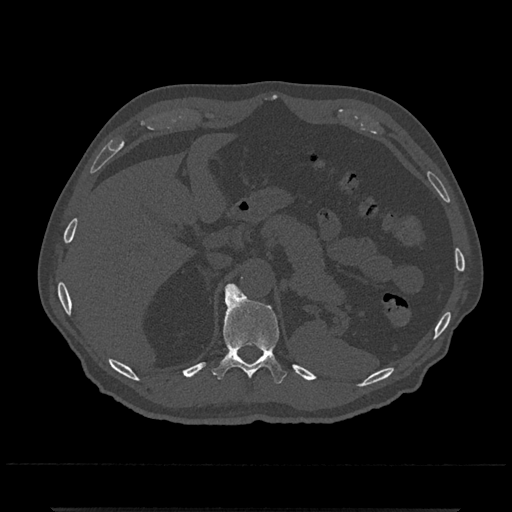
CT including the spine, one axial slice. Slice 491 of 797 in the series (ordered by position). Reconstruction kernel Br40s/3. 120 kVp. Bone window (W 1800 / L 400 HU). 0.5 mm slice thickness. 512 × 512 image matrix, field of view 393 × 393 mm. Patient: male, 67 years. From the clinical record (not read from this slice): primary cancer: prostate.
Structures marked on this image (semi-automatic segmentation, software-assisted and operator-edited):
- T11 vertebra: bounding box [x1, y1, x2, y2] px = [212, 284, 287, 384]
- T12 vertebra: [237, 288, 240, 290]